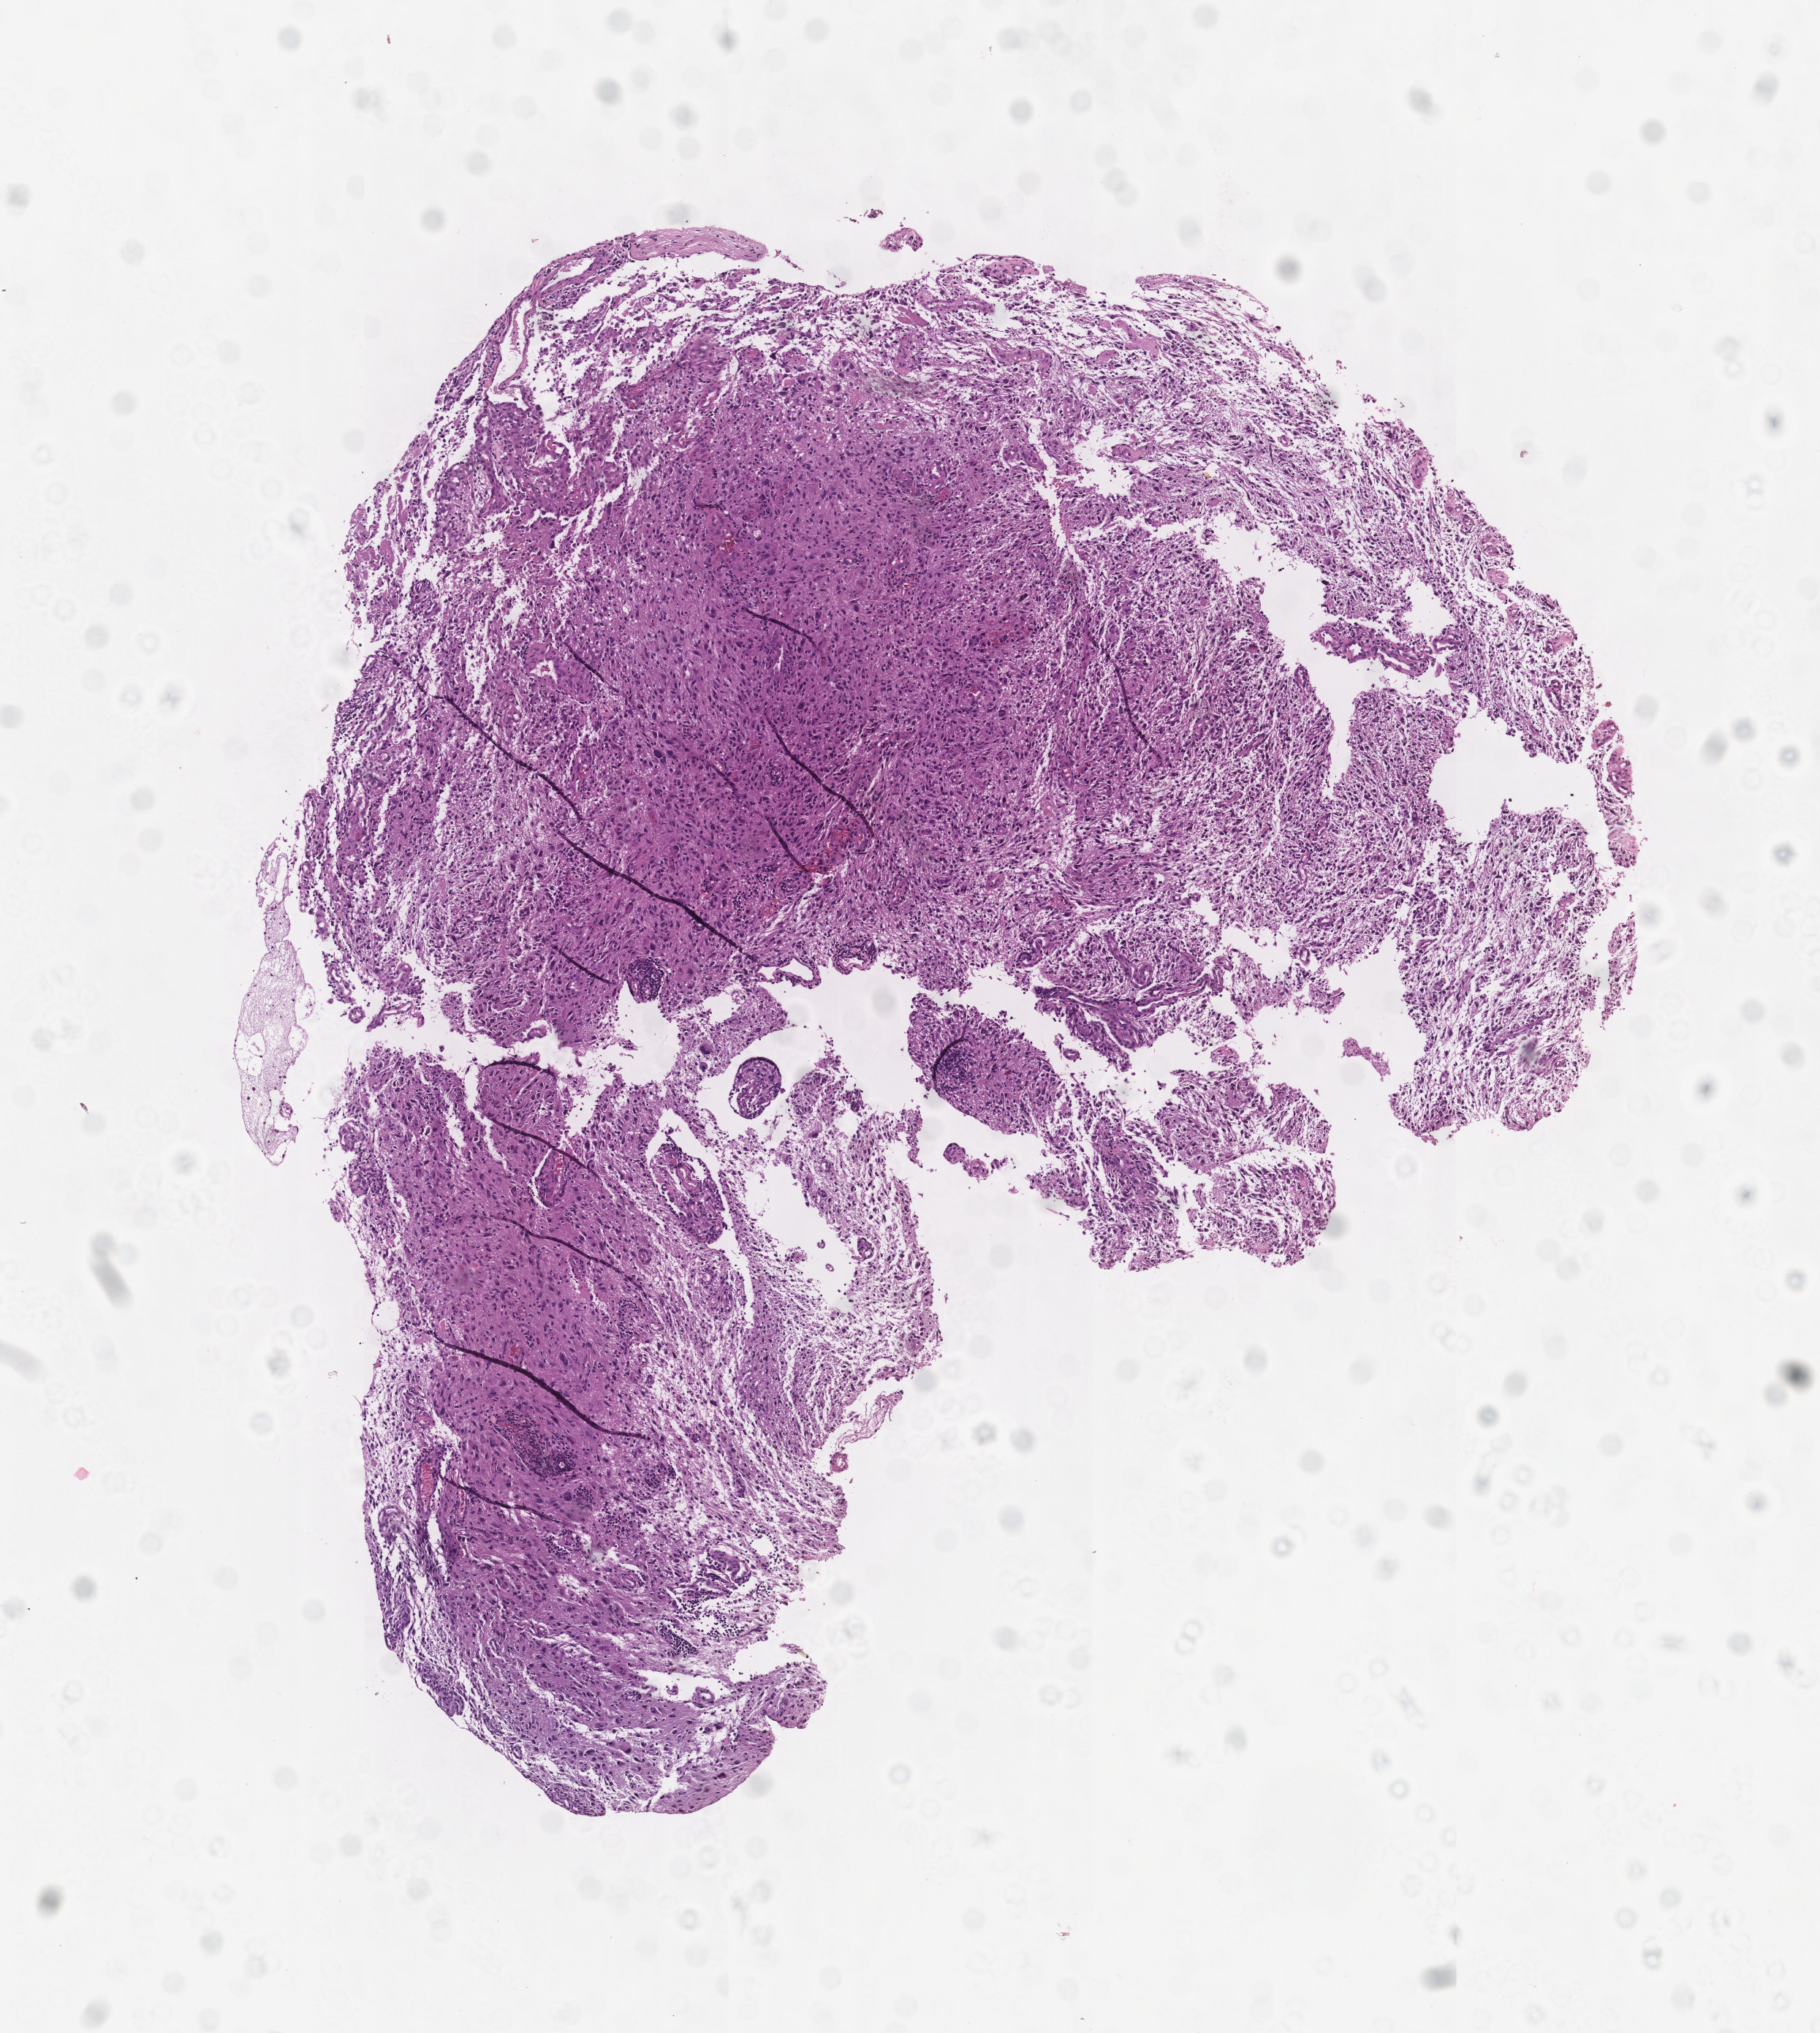
Digitized H&E-stained tissue section (whole slide) — shown as a low-resolution overview of the whole scanned area (about 5.0 x 5.6 mm, slide scanned at 20x). Brain, tumour tissue. 48-year-old female patient.
Diagnosis: Glioblastoma. Primary tumour site (as recorded): temporal lobe.